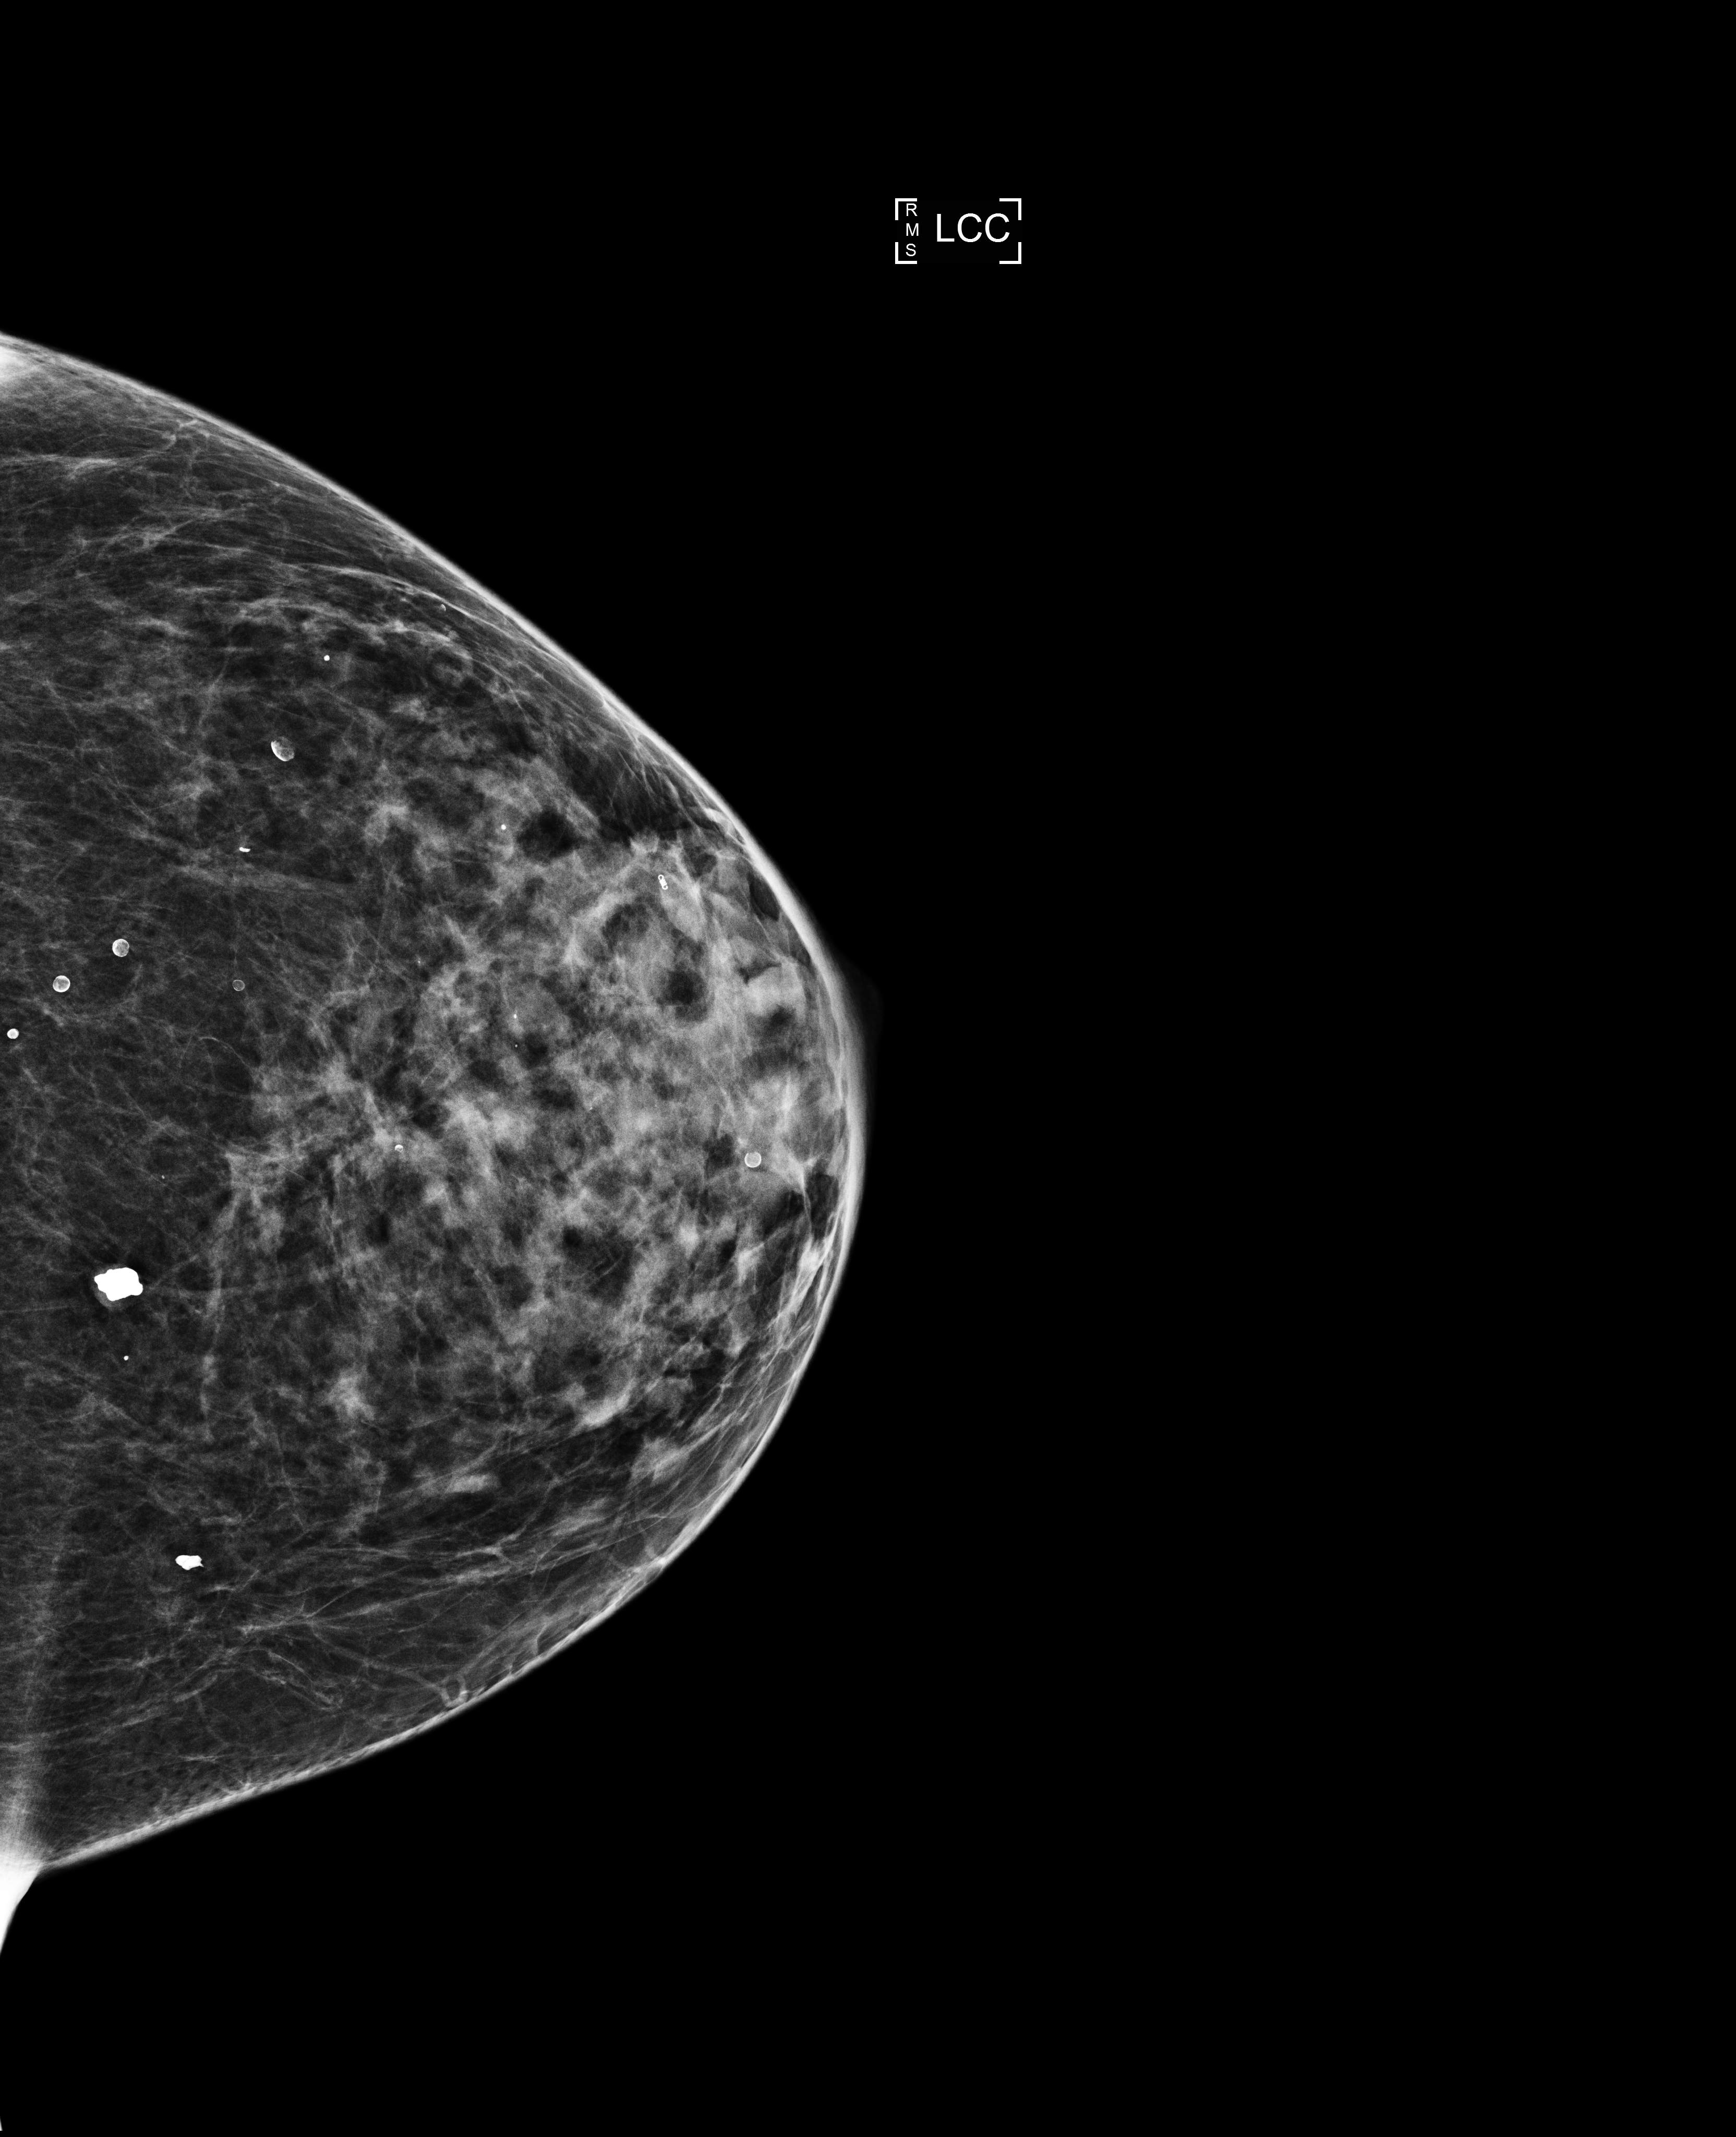
Full-field digital mammogram (FFDM); left breast; cranio-caudal projection; screening examination; compressed breast thickness 39 mm. Female patient, age 68 years.
Breast density at the screening exam (both breasts): heterogeneously dense (BI-RADS density category c). Final BI-RADS assessment for this screening round (tomosynthesis exam, both breasts): category 1. Recall: no recall after this screen.